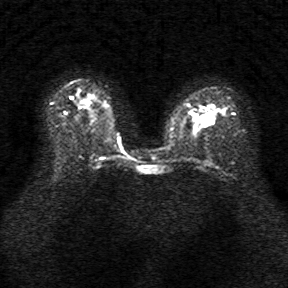
Breast MRI, one axial slice; diffusion-weighted series; image 2 of 4 stored at this slice position (different b-values; order by instance number); 1.5 T; 5 mm slice thickness; 288 × 288 image matrix. Female patient.
Annotated regions visible in this slice (expert manual segmentation):
- tumour on diffusion-weighted imaging: bounding box (x1, y1, x2, y2) in pixels: (201, 116, 210, 123)